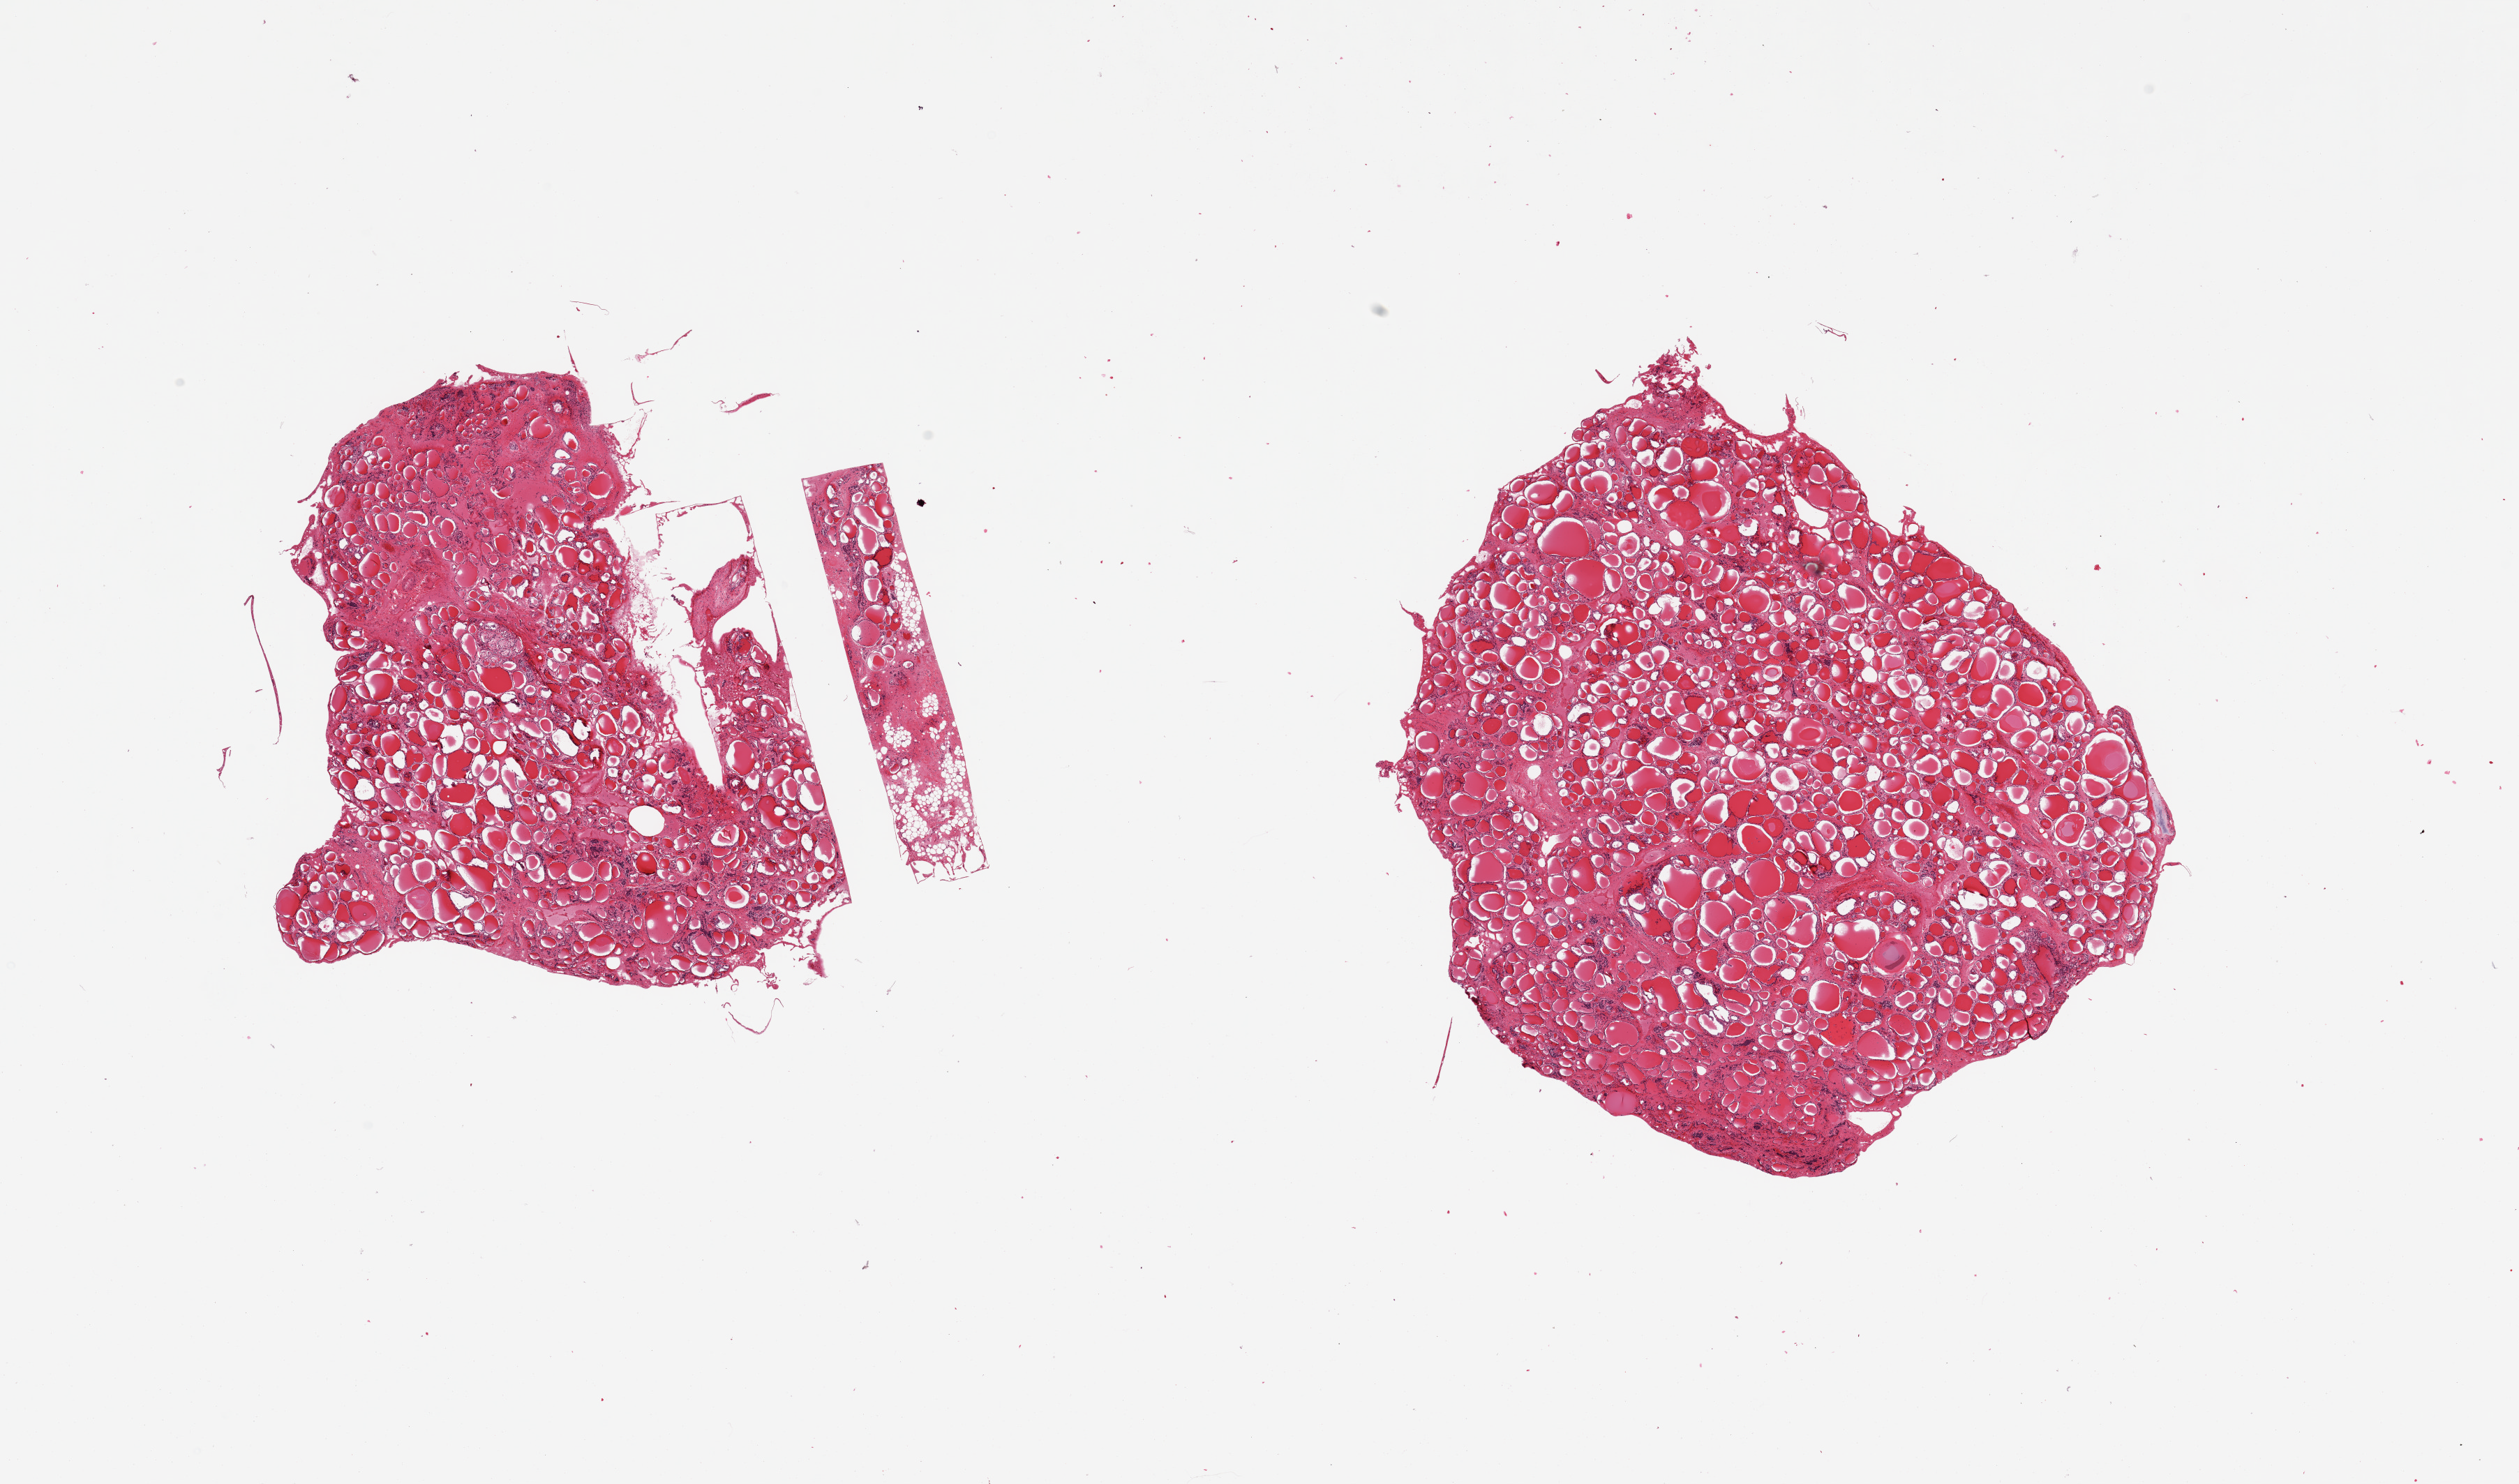
Digitized haematoxylin and eosin-stained section, shown as a low-resolution overview of the whole scanned area (about 28.5 x 16.8 mm); PAXgene-fixed, paraffin-embedded tissue; sampled site (target tissue): thyroid; tissue donor sample.
* review note (as recorded): 2 pieces, small focus of cartilage at edge of one piece